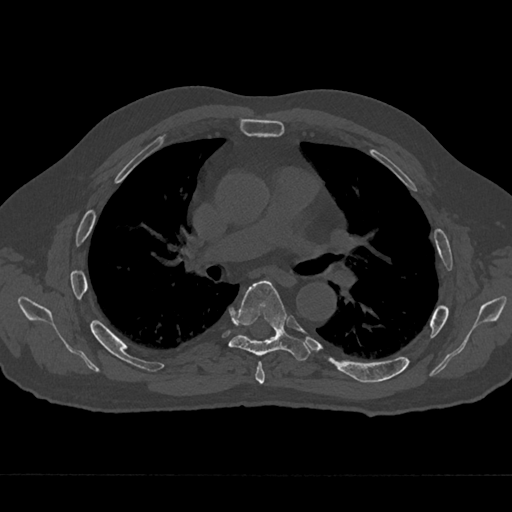
CT including the spine, one axial slice; slice 426 of 797 in the series (ordered by position); 120 kVp; bone window (W 1800 / L 400 HU); 0.5 mm slice thickness; 512 × 512 image matrix, field of view 377 × 377 mm. Patient: male, 75 years. From the clinical record (not read from this slice): primary cancer: renal; vertebrae with lytic lesions (as recorded): T4.
Structures marked on this image (semi-automatic segmentation, software-assisted and operator-edited):
- T5 vertebra: bounding box [x1, y1, x2, y2] px = [255, 361, 265, 385]
- T6 vertebra: [228, 280, 309, 361]